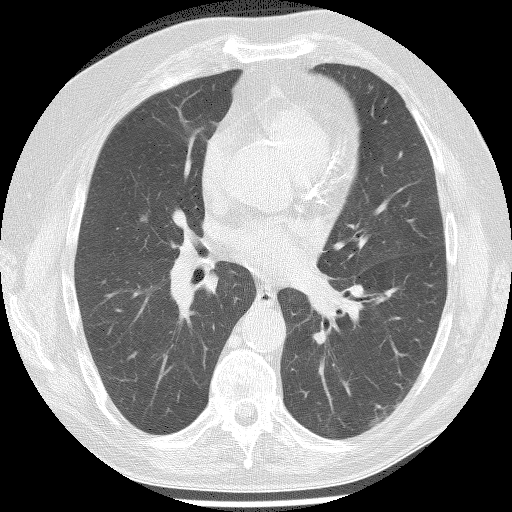
Low-dose screening chest CT, axial slice. Second screening round (one year after baseline). Lung window (W 1500 / L -600 HU). Slice 76 of 149 in the series. 512 × 512 image matrix. Male participant, aged 61 years at enrolment. Current smoker at enrolment.
Expert-annotated lung lesion, bounding box [x1, y1, x2, y2] px = [123, 201, 158, 237]. The screening reader recorded 2 non-calcified nodules or masses ≥4 mm on this exam; which of them this box marks is not recorded. Participant outcome: lung cancer diagnosed 147 days after this screen — bronchiolo-alveolar adenocarcinoma, NOS, right middle lobe, well differentiated (G1), stage IA (AJCC 6th edition), 15 mm at pathology.